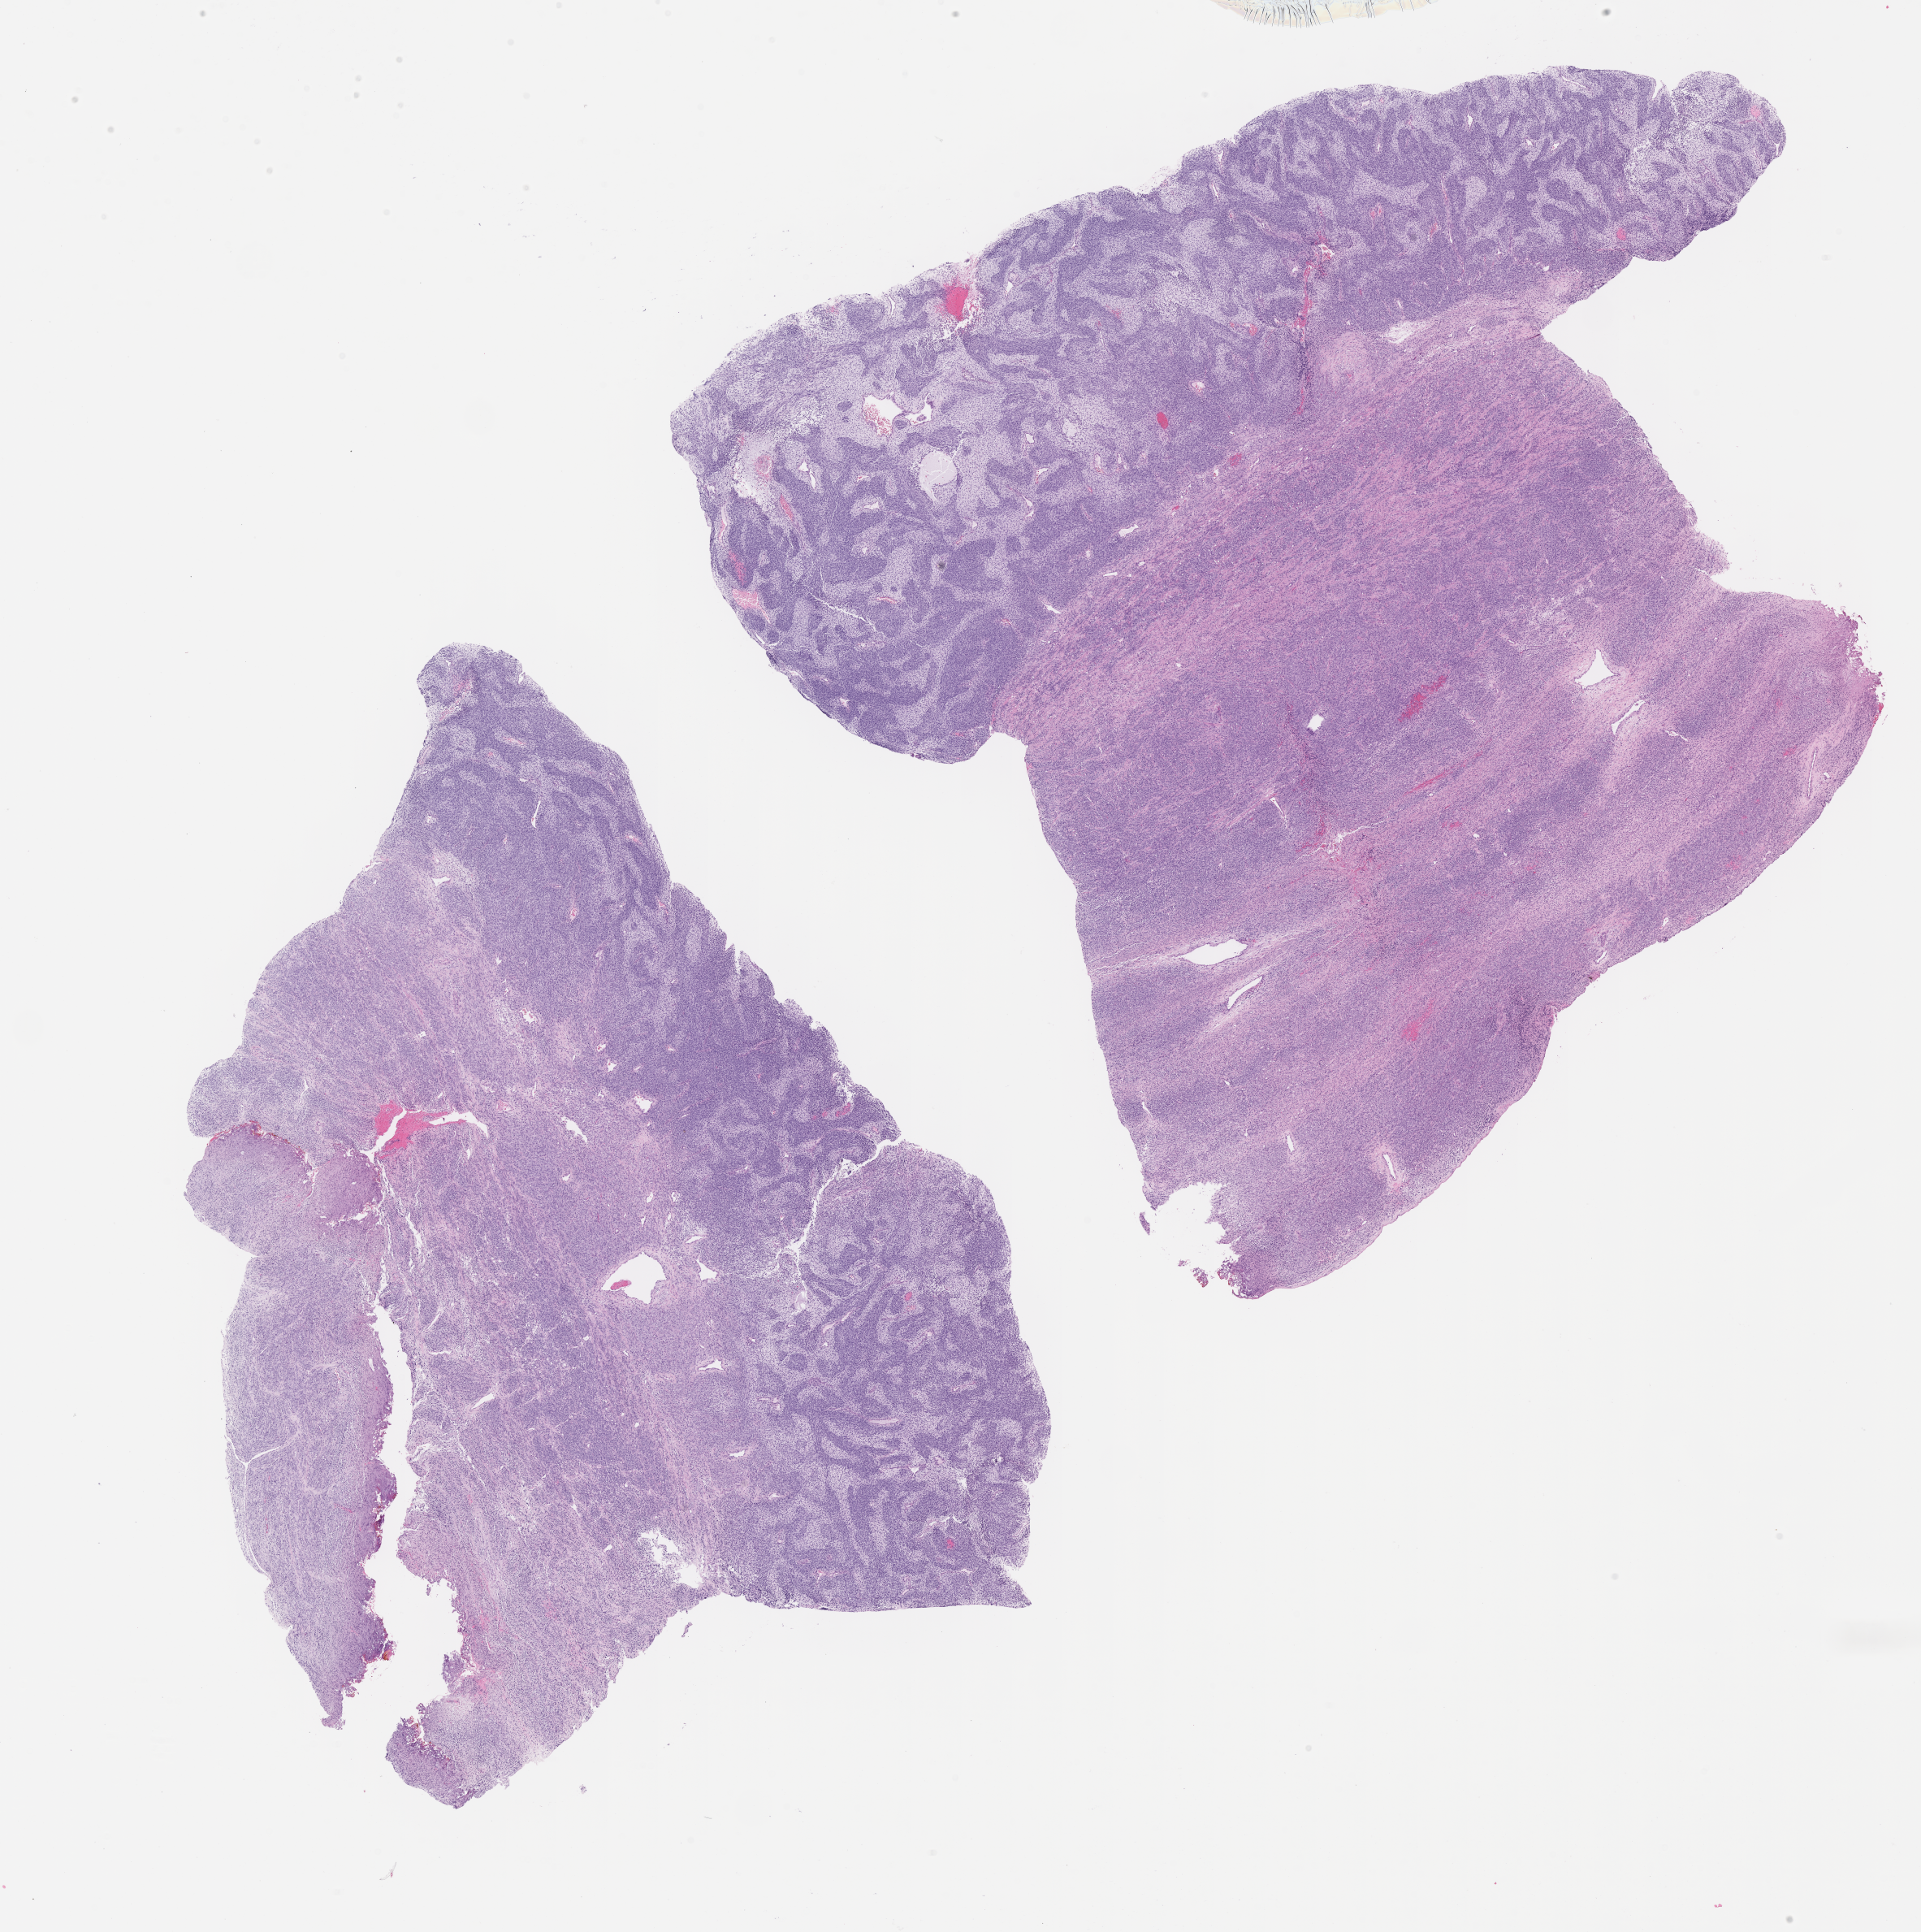
Digitized H&E-stained section of tumor tissue, low-resolution overview of the scanned area, about 19.1 x 19.2 mm; FFPE section; sample anatomic site: abdomen. Male patient, age at diagnosis 1.1 years.
• diagnosis: rhabdomyosarcoma; histological classification: embryonal rhabdomyosarcoma
• metastatic status at presentation (as recorded): non-metastatic (confirmed)
• primary site (case record): pelvis, site indeterminate
• stage (as recorded): 1